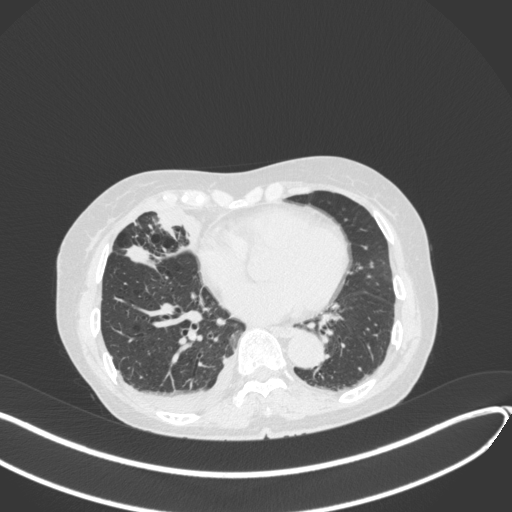
Chest CT, one axial slice; 120 kVp; lung window (W 1500 / L -600 HU); 1 mm slice thickness; 512 × 512 image matrix. Female patient, age 75 years. From the clinical record (not read from this slice): clinical TNM (as recorded): T2a N3 M0.
Outlined on this slice (rectangle marked by the reading radiologist):
- lung tumour (recorded histology: adenocarcinoma): bounding box [x1, y1, x2, y2] px = [121, 242, 152, 266]